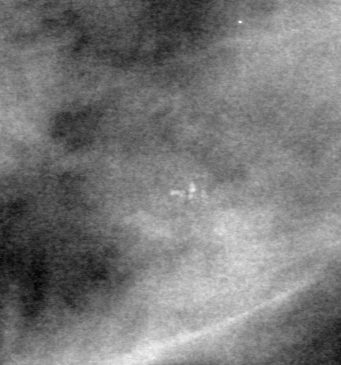
Region of interest cut from a scanned film mammogram (one marked finding), right breast, MLO view, BI-RADS breast density category 3 (scale 1–4).
- Calcifications, morphology amorphous, distribution segmental; BI-RADS assessment category 0 (incomplete: needs additional imaging); subtlety rating 3 on a 1 (subtle) to 5 (obvious) scale; pathology (as recorded): benign.